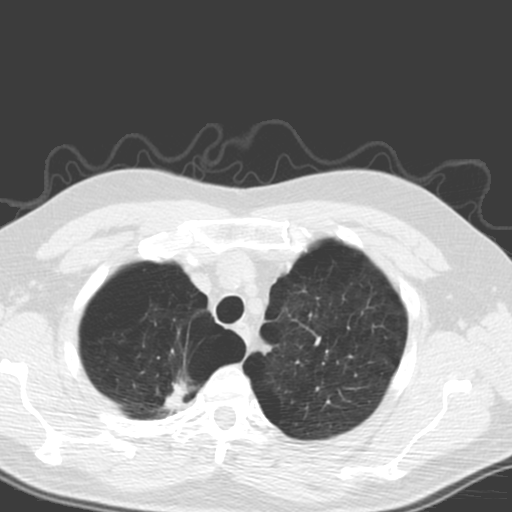
Low-dose screening chest CT, one axial slice; position 144 of 173 along the scan axis; lung window (W 1500 / L -600 HU); 3.2 mm slice thickness; 512 × 512 image matrix, field of view 340 × 340 mm.
Annotated regions visible in this slice (manually delineated by an expert):
- lesion 1 (tumor, upper lobe of right lung): bounding box <162,379,195,411> (left, top, right, bottom; pixels)